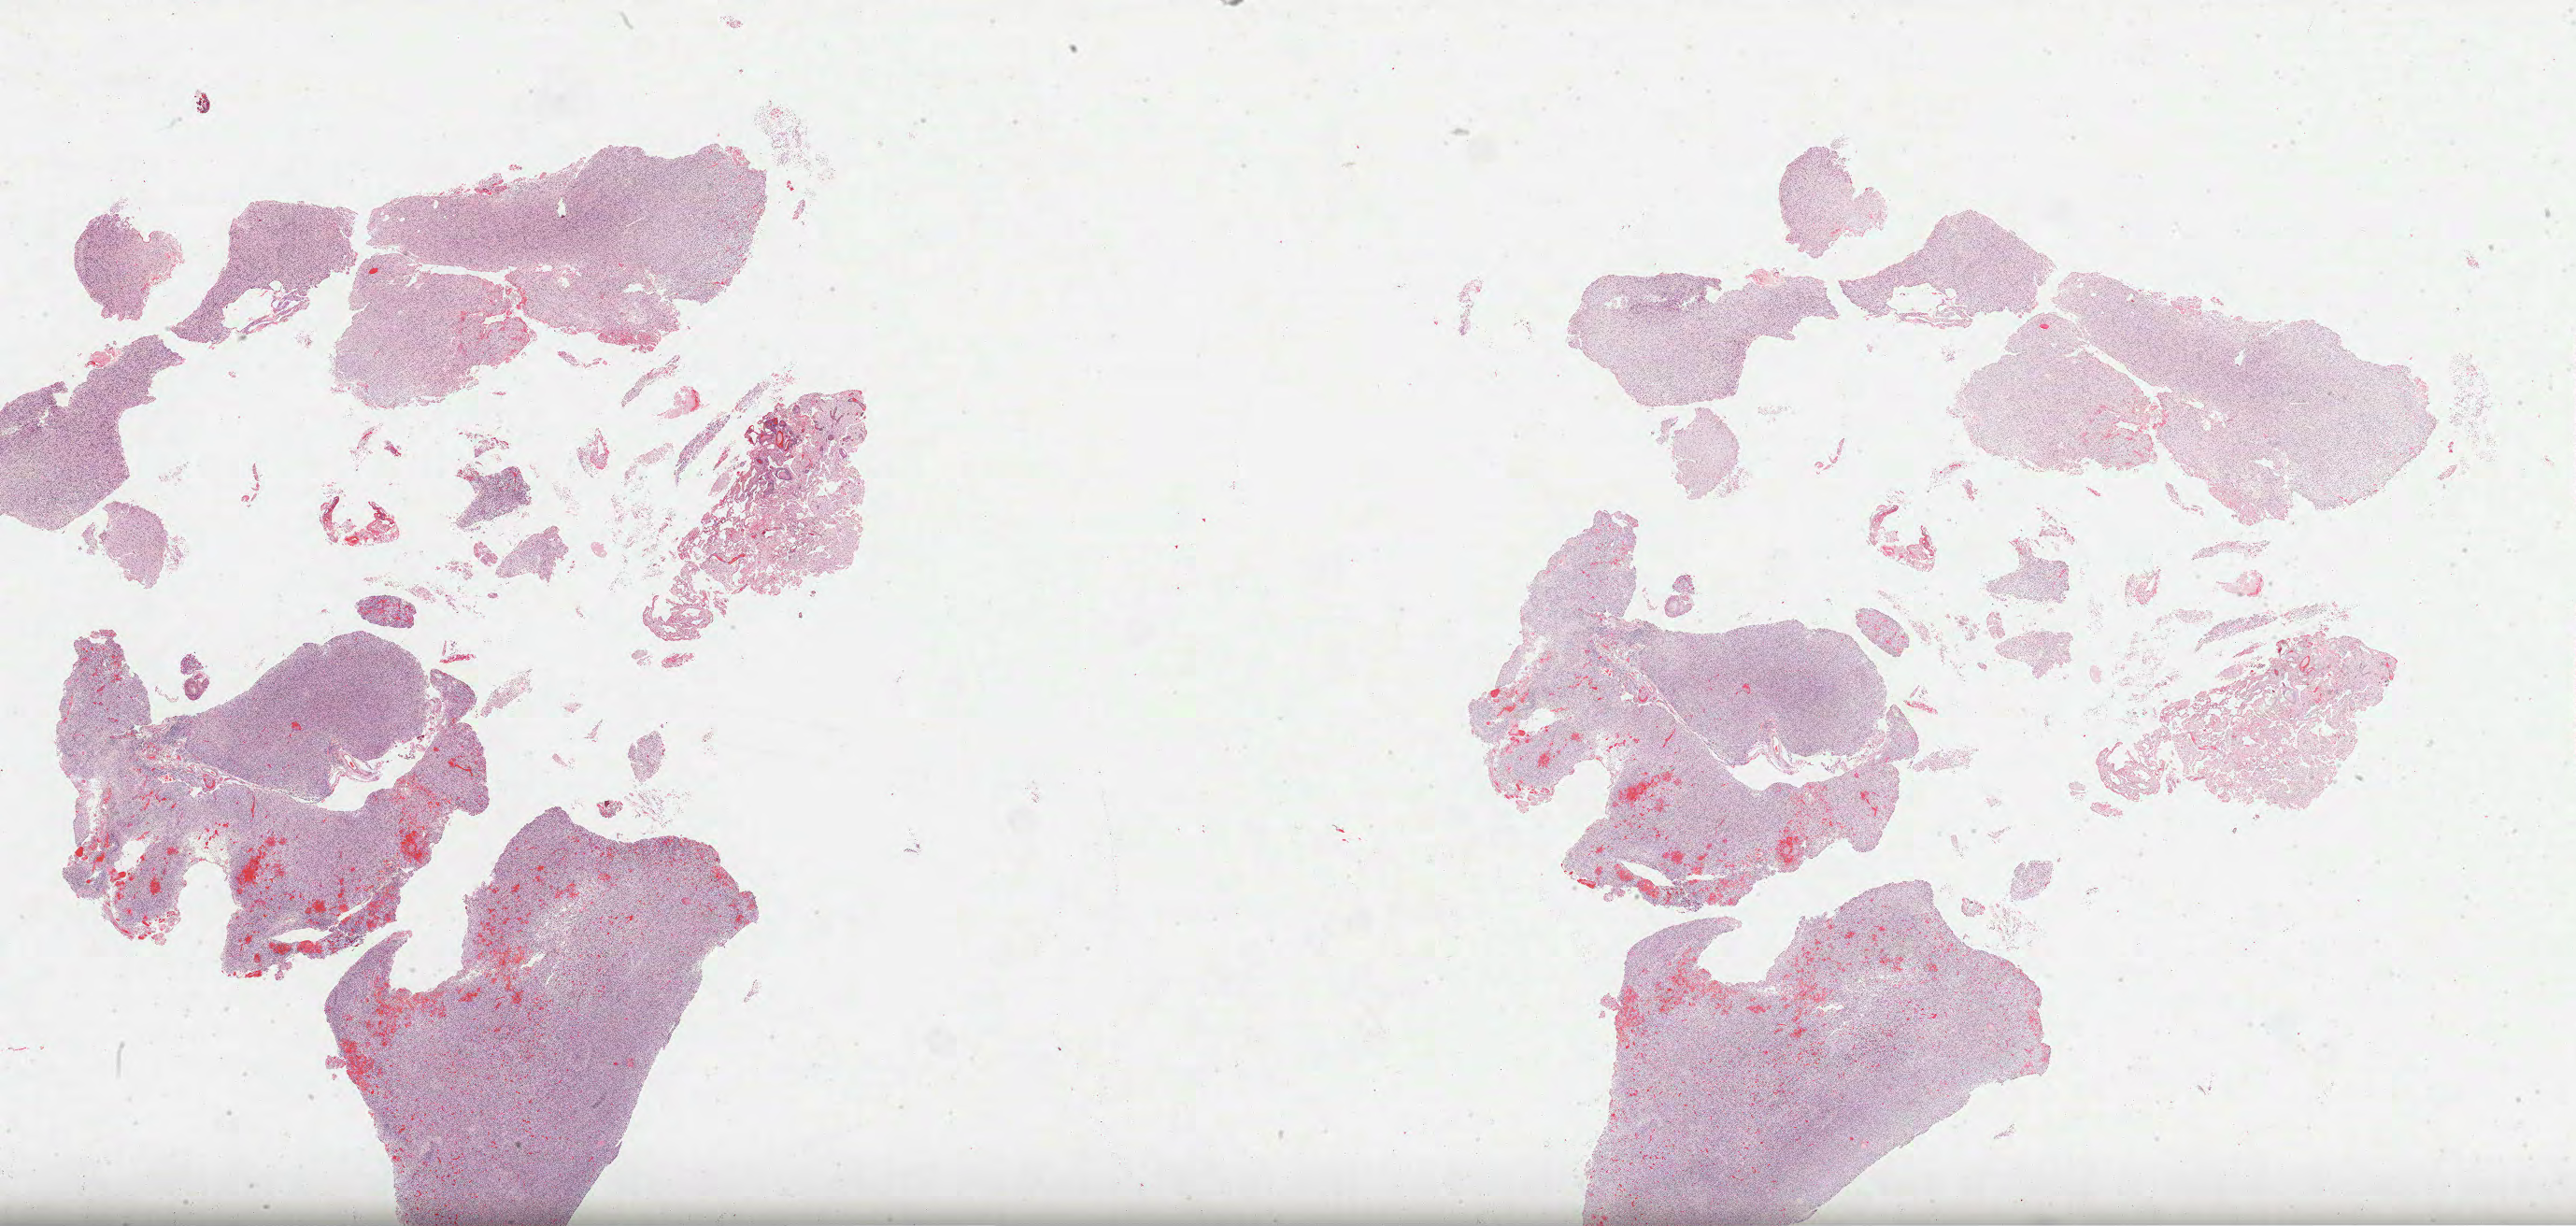
H&E-stained whole-slide image, whole scanned area (about 44.5 x 21.2 mm, slide scanned at 40x) shown as a low-resolution overview, formalin-fixed paraffin-embedded (FFPE) diagnostic section, sample: primary tumour, brain. Female patient; age at initial diagnosis 77 years.
Pathologic diagnosis: Glioblastoma.